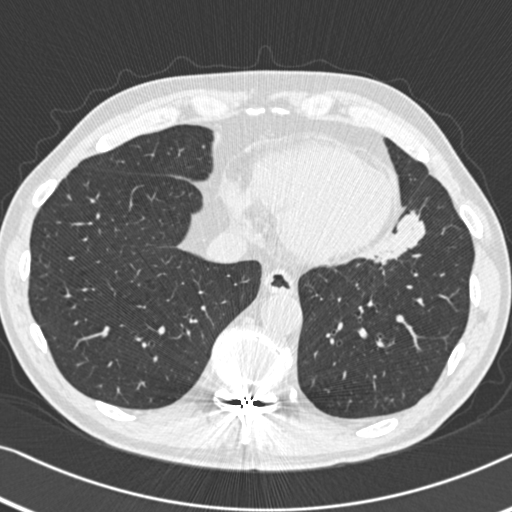
Low-dose screening chest CT, one axial slice; position 133 of 383 along the scan axis; reconstruction kernel B30f; lung window (W 1500 / L -600 HU); 512 × 512 image matrix.
Outlined on this slice (expert manual segmentation):
- lesion 1 (tumor, upper lobe of left lung): bounding box (x1, y1, x2, y2) in pixels: (377, 212, 425, 265)